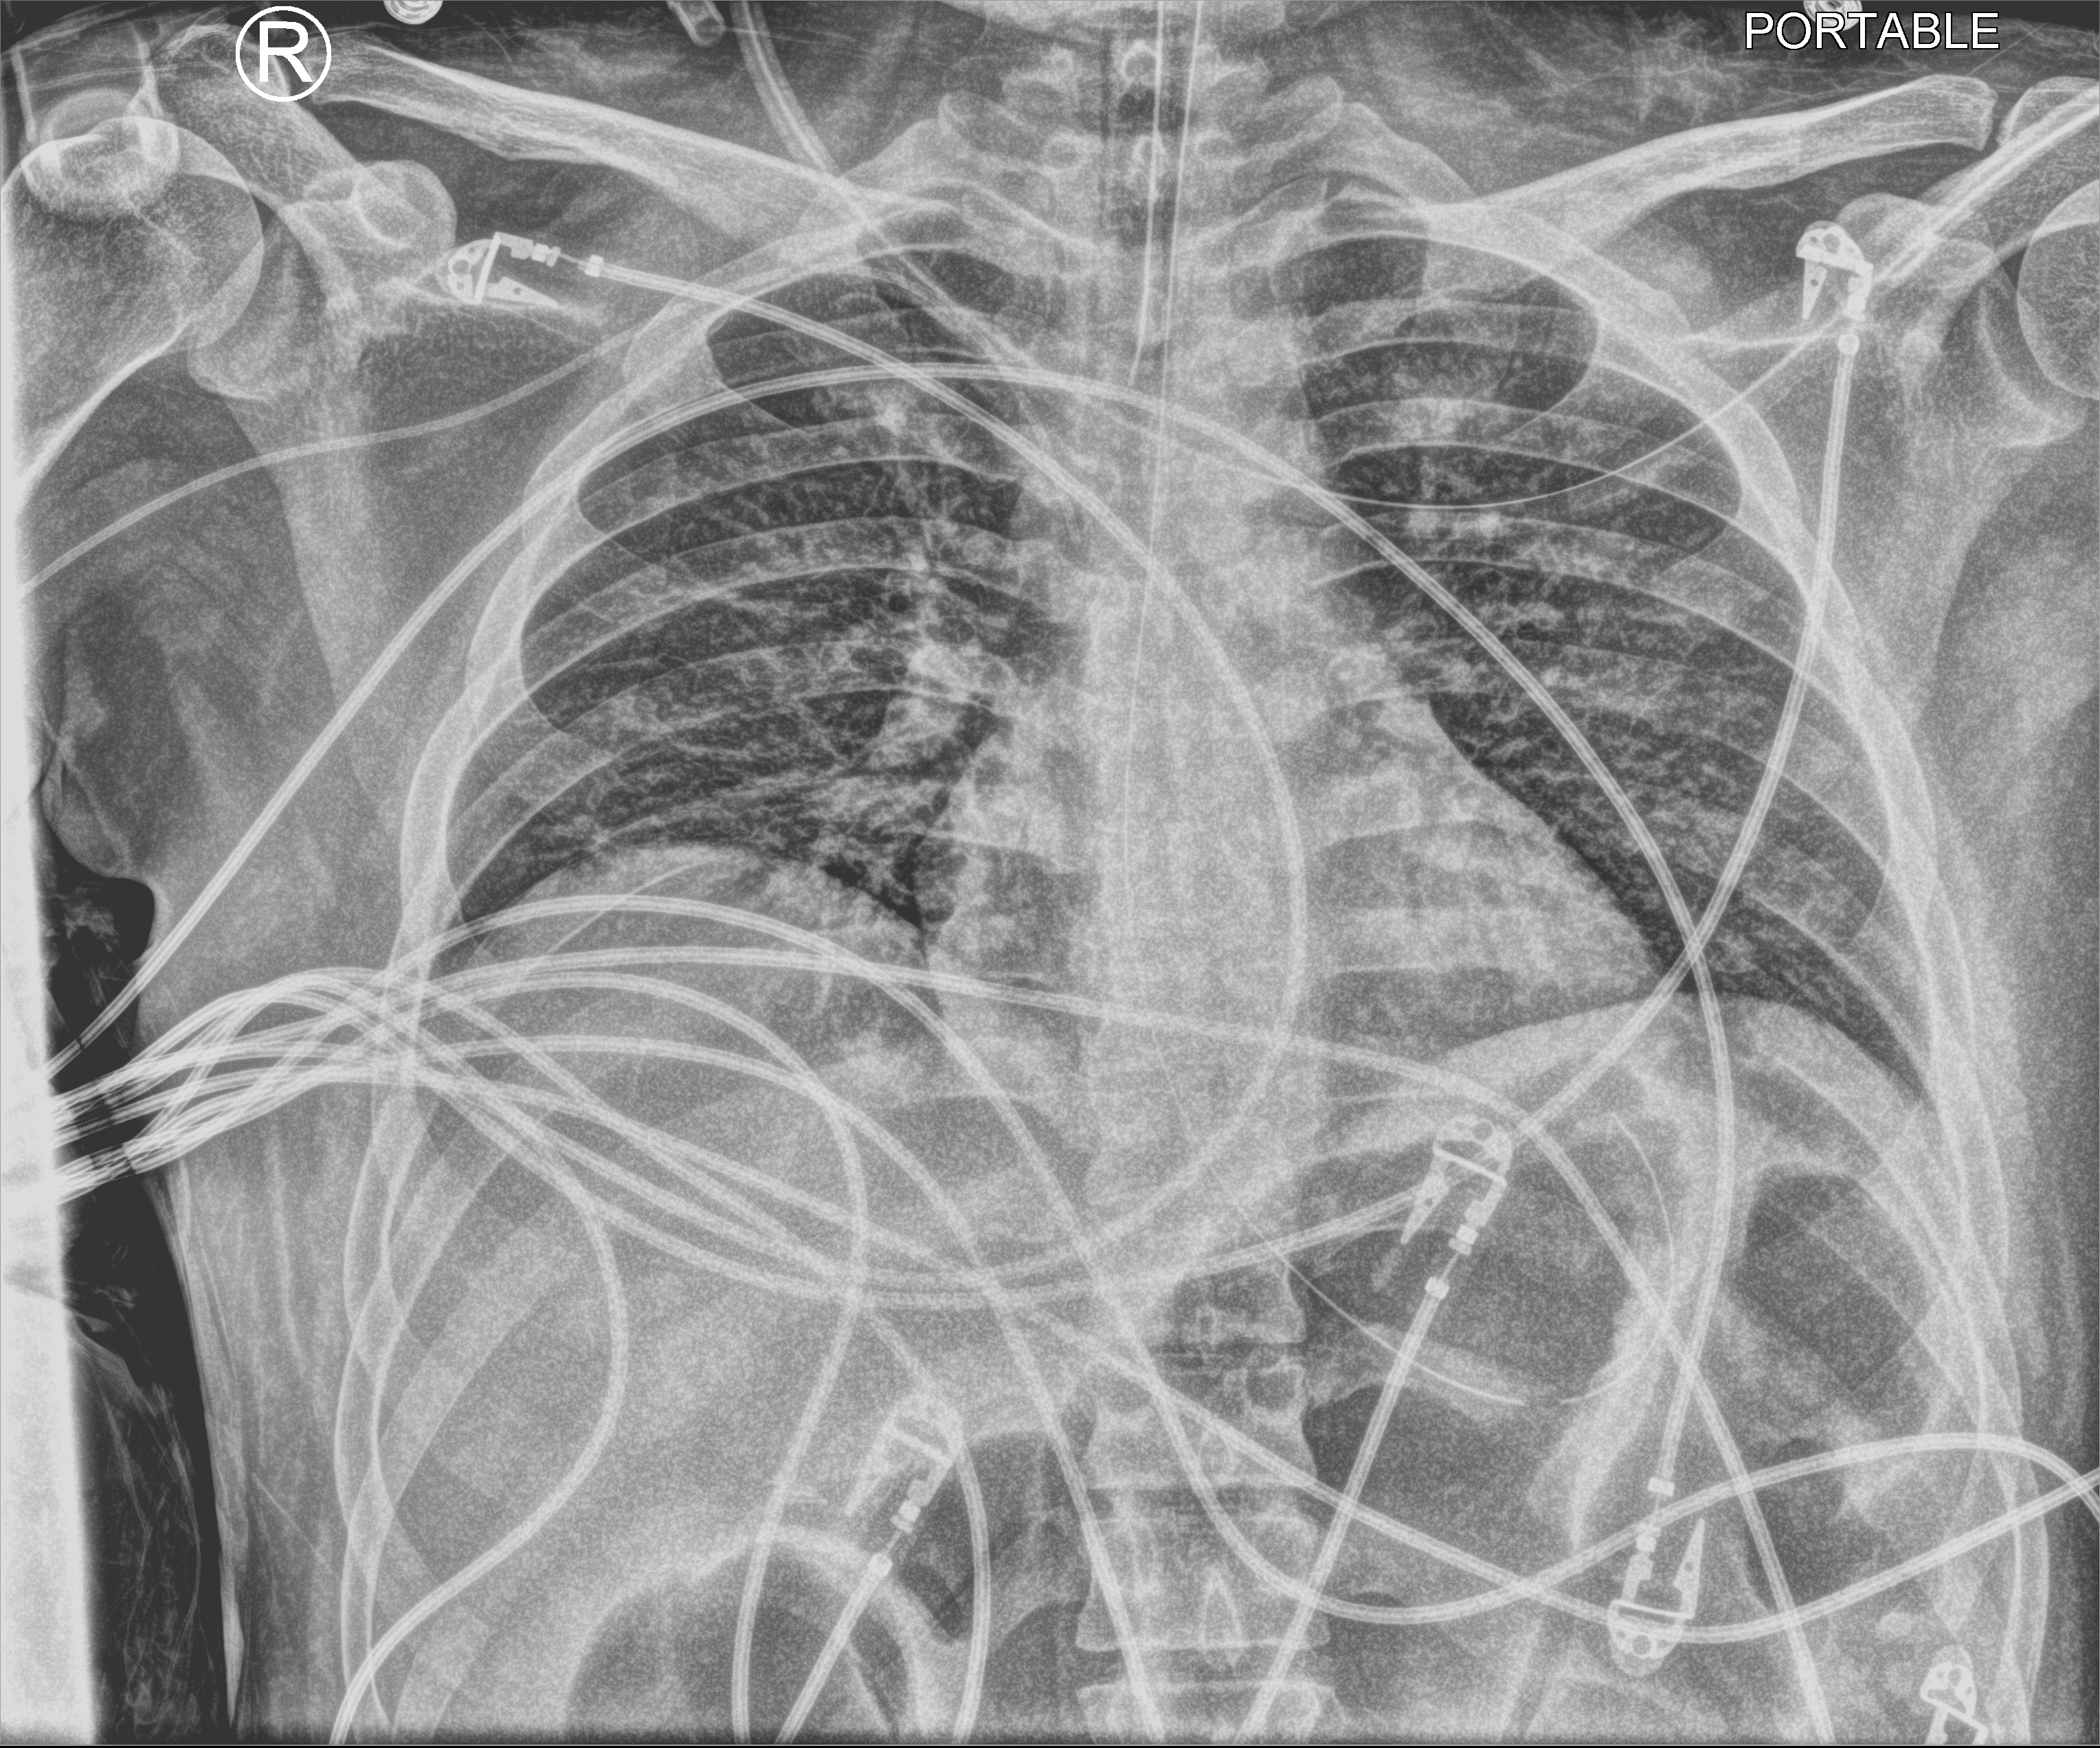
Bedside chest radiograph (computed radiography), anteroposterior (AP) projection. Male patient hospitalised with COVID-19, age 18–59 years.
Admission-level facts for this patient (not findings on this image; timing relative to this image not recorded):
- length of hospital stay: 44 days
- hypertension (admission record): no